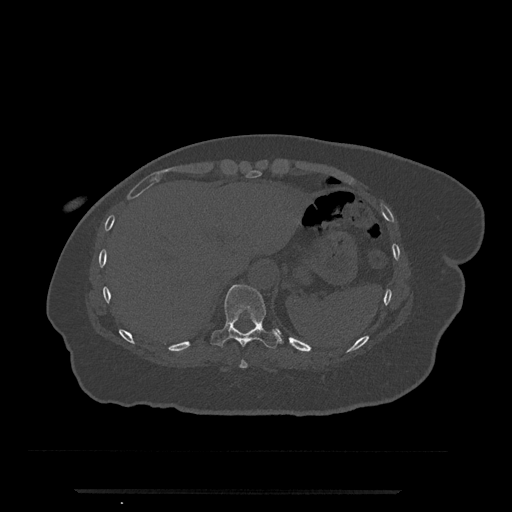
CT including the spine, one axial slice; slice 290 of 797 in the series (ordered by position); bone window (W 1800 / L 400 HU); 0.5 mm slice thickness; 512 × 512 image matrix, field of view 440 × 440 mm. Patient: female, 51 years. Case-level facts recorded for this patient, not image findings: primary cancer: neuro.
Outlined on this slice (semi-automatically segmented with operator editing):
- T10 vertebra: bounding box [x1, y1, x2, y2] px = [211, 285, 280, 349]
- T9 vertebra: [239, 359, 248, 369]